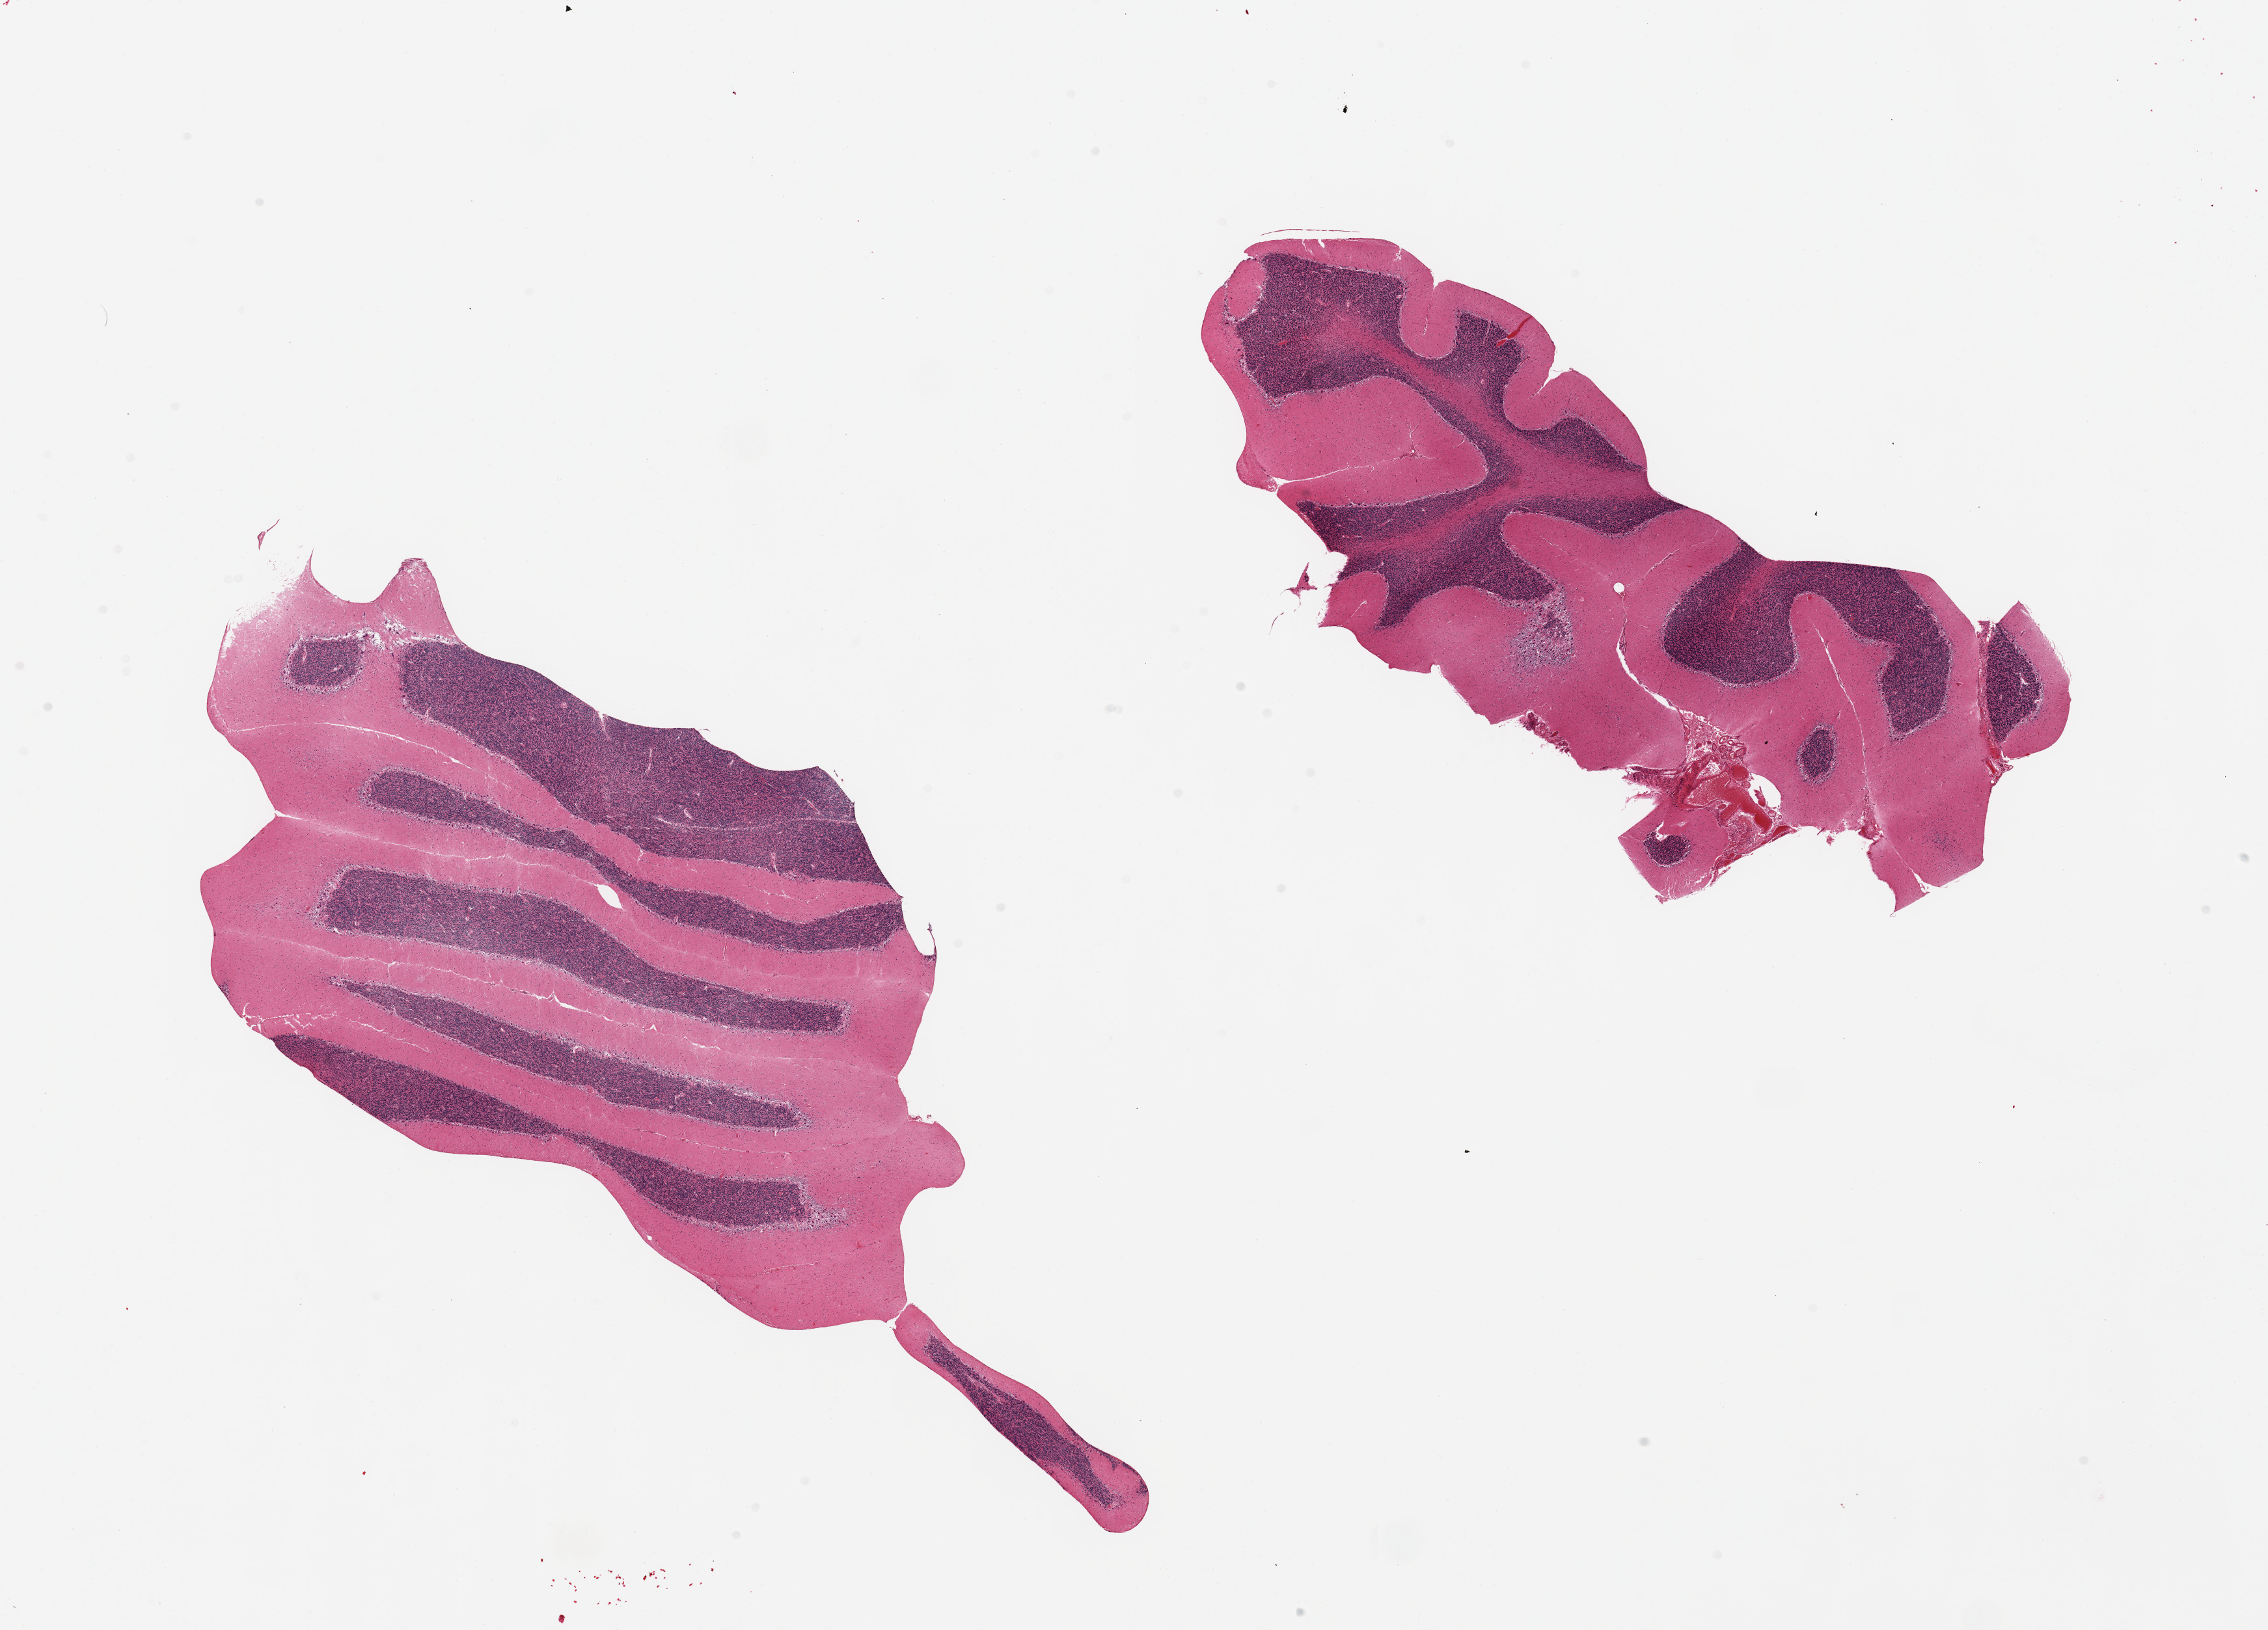
H&E whole-slide image, a low-resolution overview of the entire scanned area, about 27.6 x 19.8 mm (acquisition: 20x scan), PAXgene-fixed, paraffin-embedded tissue, sampled site (target tissue): cerebellum, donor tissue sample. Donor: male.
- review note (as recorded): 2 pieces; well preserved Purkinje cells